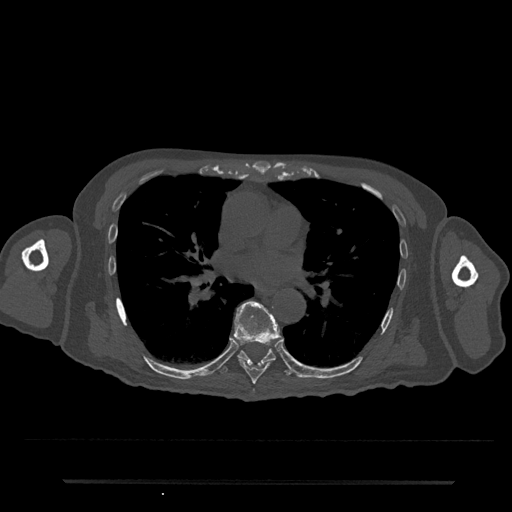
CT including the spine, one axial slice; position 456 of 797 along the scan axis; reconstruction kernel Br40s/3; 120 kVp; bone window (W 1800 / L 400 HU); 0.5 mm slice thickness; 512 × 512 image matrix. Male patient, age 74 years. From the clinical record (not read from this slice): primary cancer: prostate.
Annotated regions visible in this slice (semi-automatically segmented with operator editing):
- T6 vertebra: box from (x=253, y=389) to (x=255, y=392) px
- T7 vertebra: (x=234, y=301)–(x=283, y=385)
- T8 vertebra: (x=221, y=349)–(x=291, y=376)